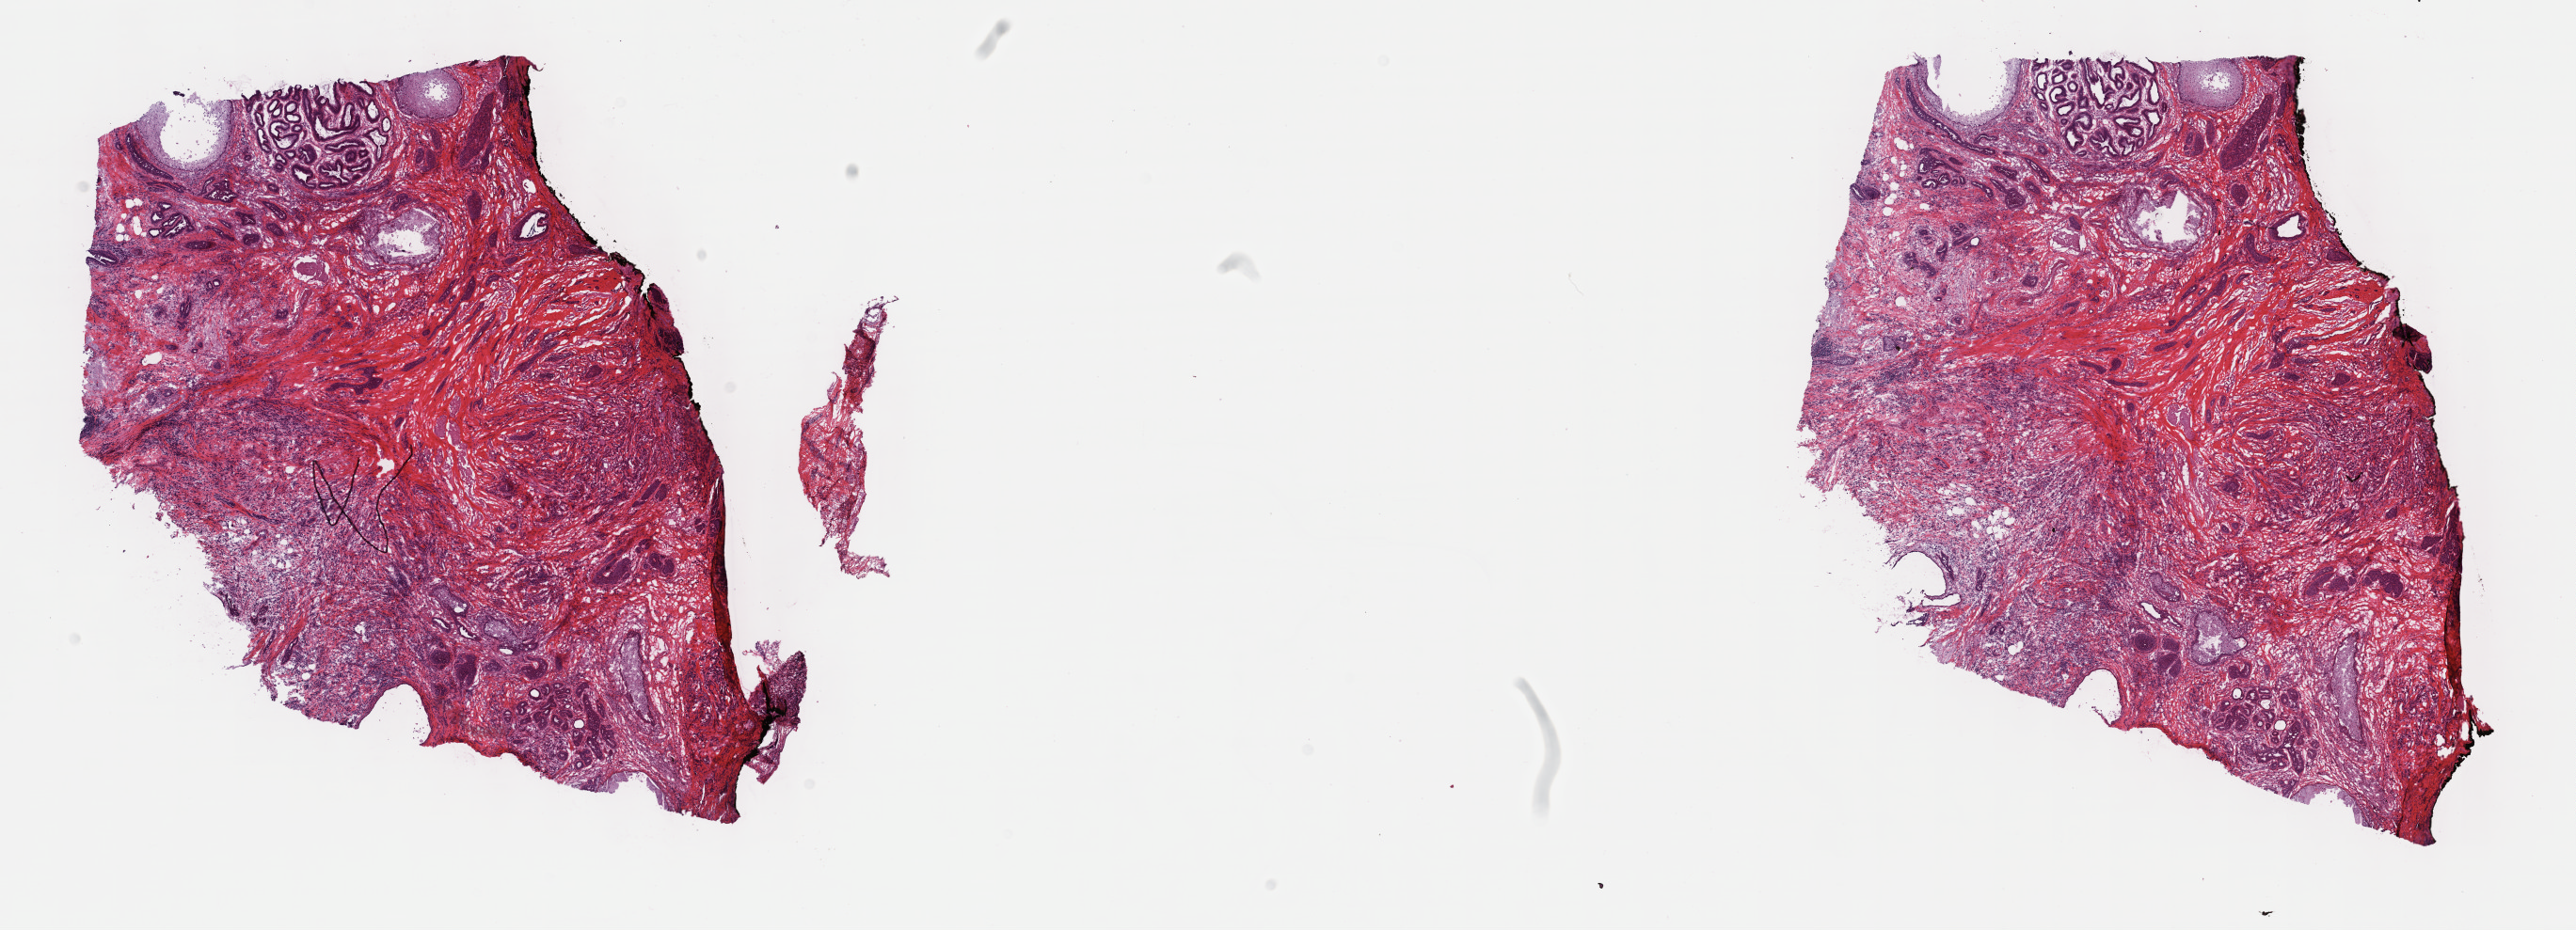
Hematoxylin and eosin (H&E) stained whole-slide image, shown as a low-resolution overview of the whole scanned area (about 22.1 x 8.0 mm). Frozen section. Primary tumour sample from the breast. Female, age 60 years at initial diagnosis. Composition of this section per pathologist review: tumour cells 70%, tumour nuclei 70%.
Diagnosis: Lobular carcinoma, NOS.